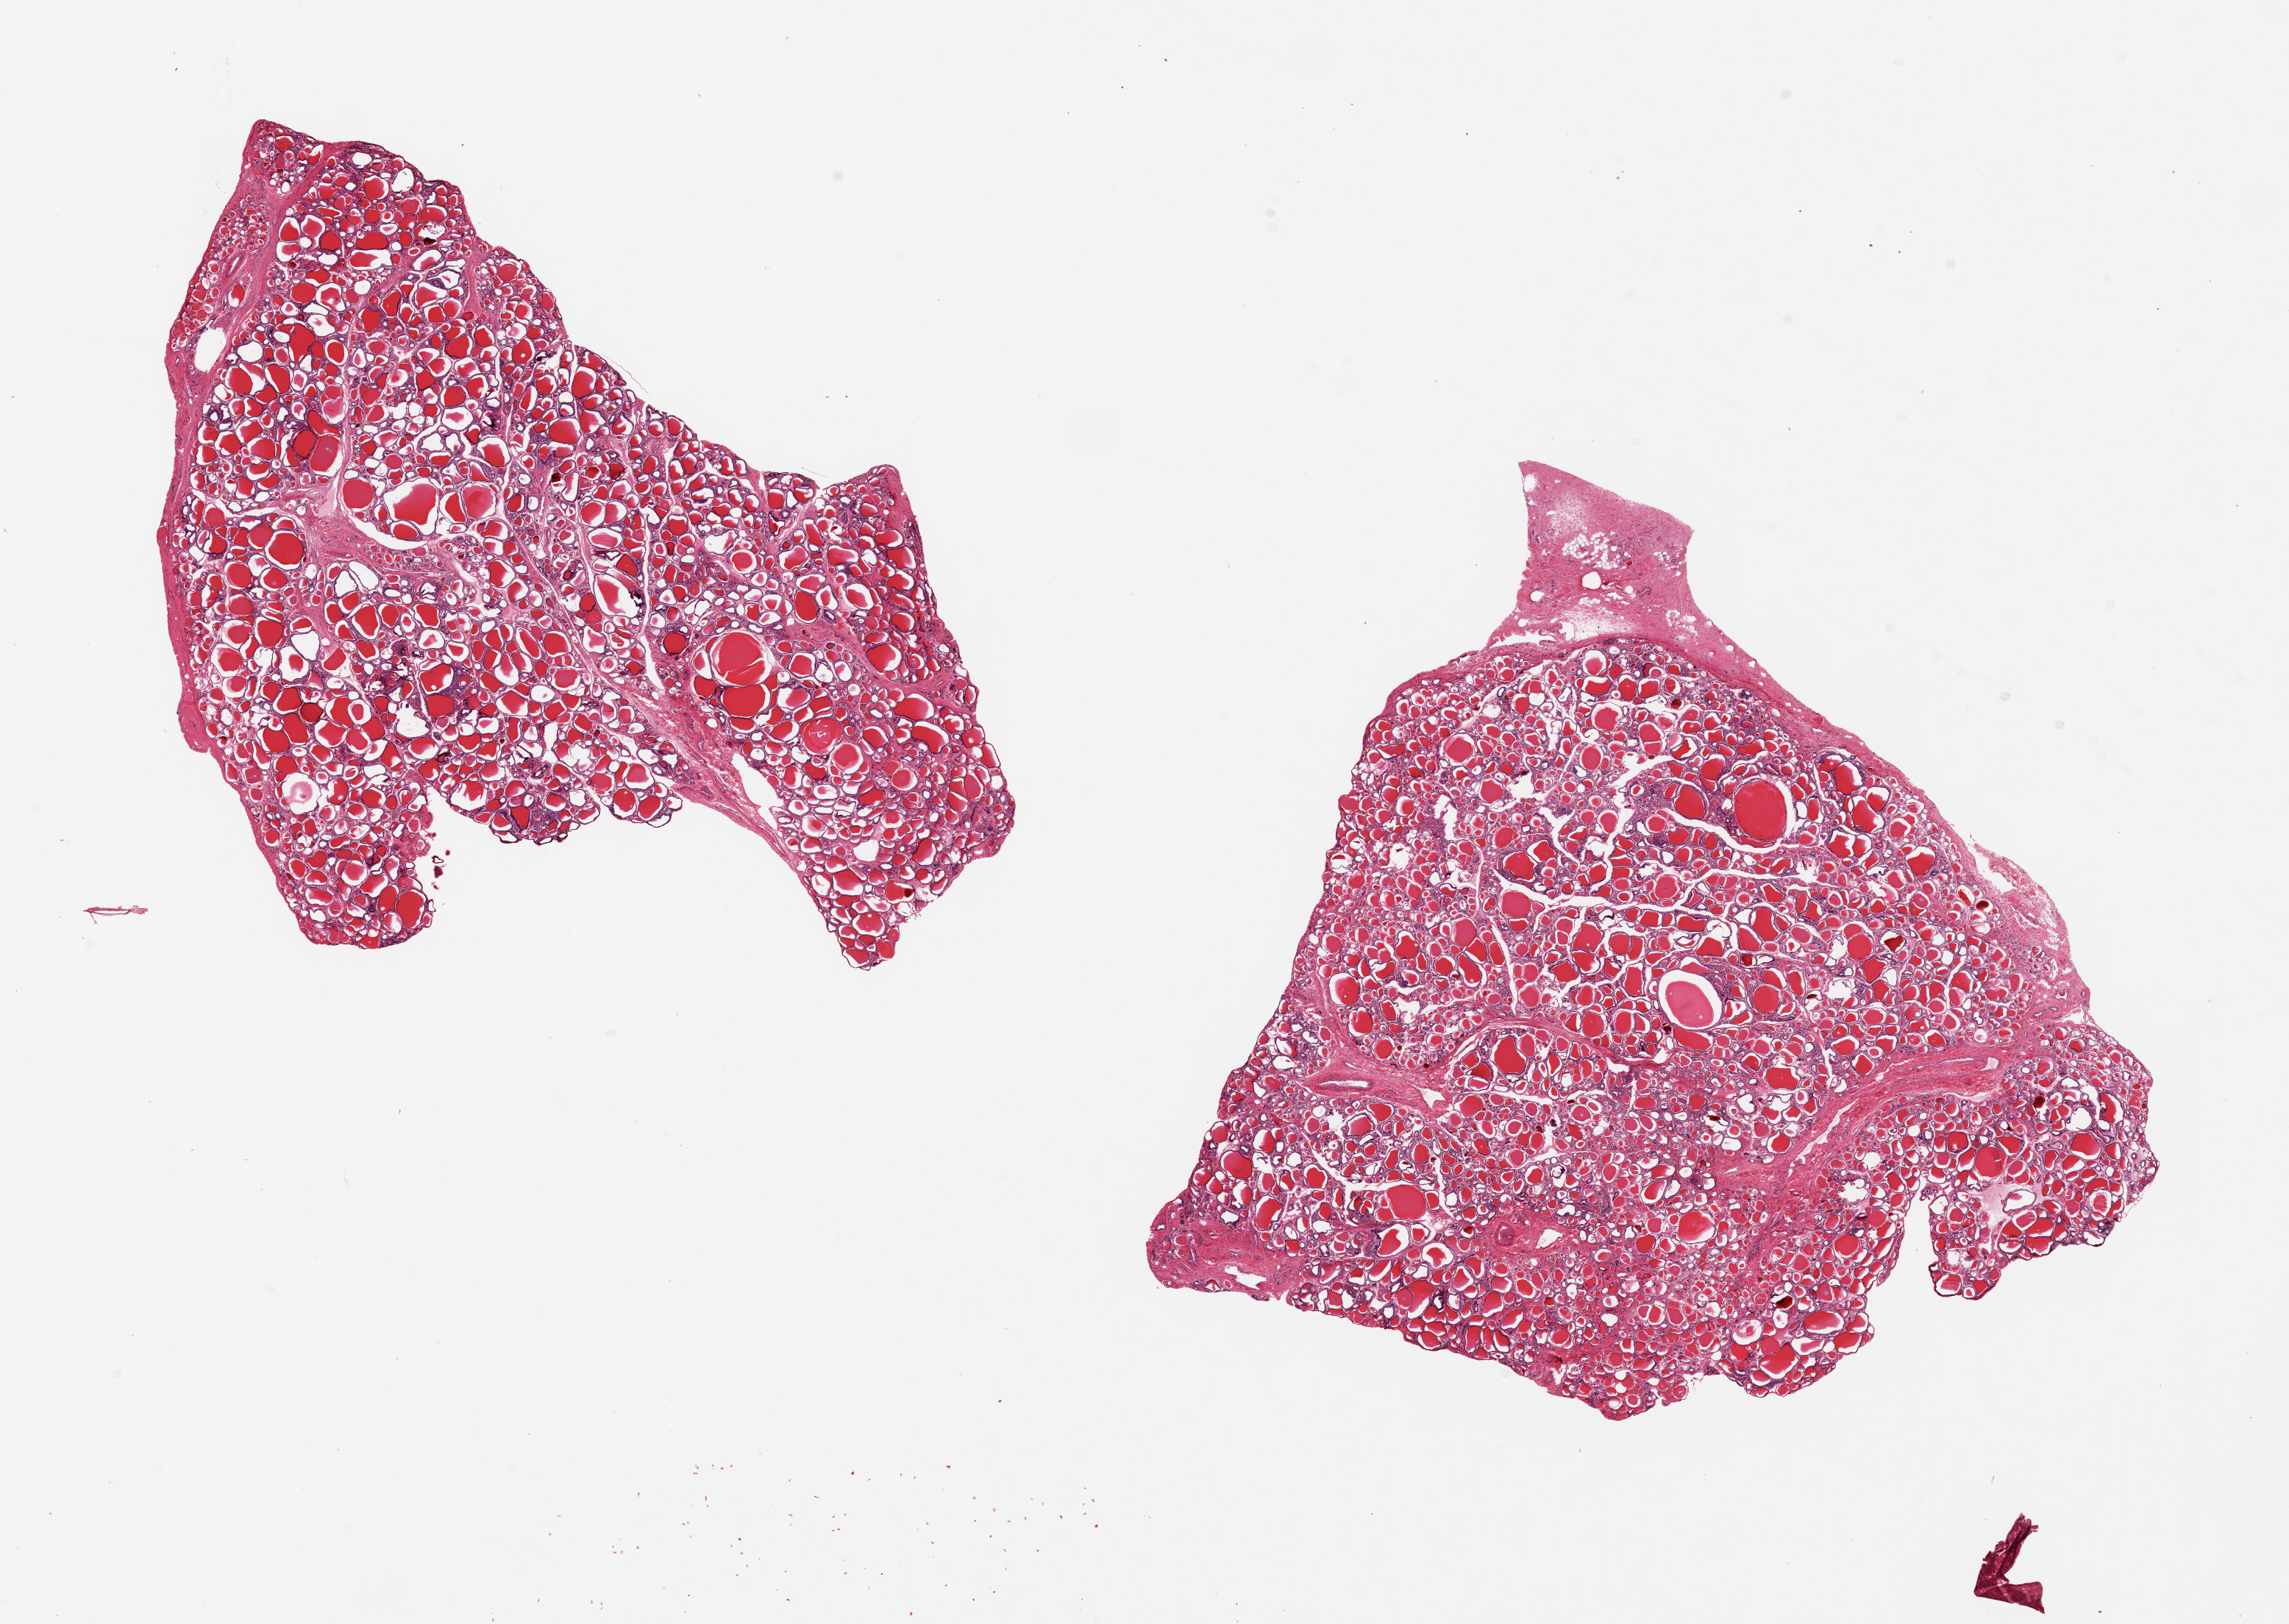
Whole-slide image, haematoxylin and eosin stain — low-resolution overview of the scanned area, about 24.6 x 17.5 mm (from a 20x scan), PAXgene-fixed paraffin-embedded (PFPE) section, section of thyroid (target tissue), tissue donor sample. Donor: female.
Reviewer comment on this tissue sample: 2 pieces, 11x7 & 10x9mm; 1x2 mm fibrous projection at 1 edge.